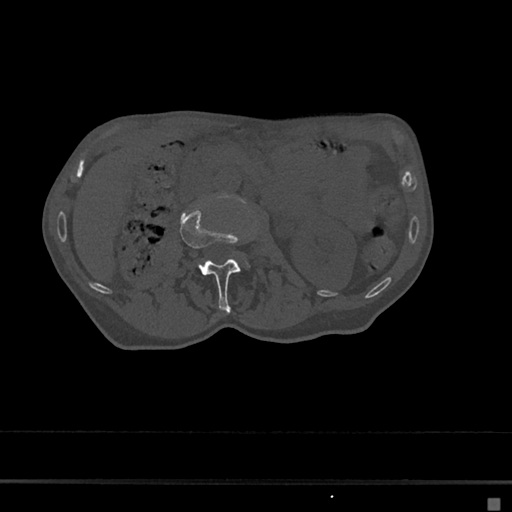
CT including the spine, one axial slice. Position 2 of 797 along the scan axis. 120 kVp. Bone window (W 1800 / L 400 HU). 0.5 mm slice thickness. 512 × 512 image matrix. Female patient, age 68 years. From the clinical record (not read from this slice): primary cancer: renal.
Structures marked on this image (semi-automatically segmented with operator editing):
- L2 vertebra: bounding box [x1, y1, x2, y2] px = [180, 207, 244, 311]